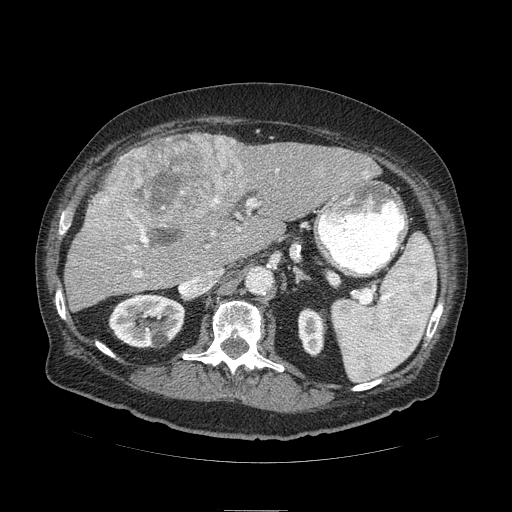
Contrast-enhanced abdominal CT (liver protocol), one axial slice; position 54 of 103 along the scan axis; 120 kVp; soft-tissue window (W 400 / L 40 HU); 512 × 512 image matrix. Case-level facts recorded for this patient, not image findings: diagnosis: hepatocellular carcinoma (patient treated with transarterial chemoembolisation; whether this scan precedes or follows treatment is not stated here); TNM stage (as recorded): Stage-IIIA; Child-Pugh class: B; tumour differentiation: well differentiated.
Annotated regions visible in this slice (semi-automatic segmentation, software-assisted and operator-edited):
- liver parenchyma outside the tumour (the mass and vessels are separate outlines, so this box may not span the whole liver): box from (x=64, y=134) to (x=378, y=310) px
- mass: (x=83, y=131)–(x=246, y=250)
- liver vessels: (x=126, y=169)–(x=279, y=278)